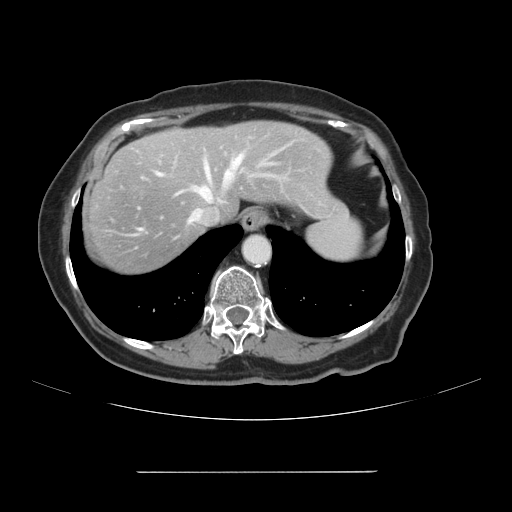
Contrast-enhanced abdominal CT, one axial slice. Position 89 of 111 along the scan axis. 120 kVp. Intravenous contrast given. Soft-tissue window (W 400 / L 40 HU). 2.5 mm slice thickness. 512 × 512 image matrix, field of view 400 × 400 mm. Female patient, age 74 years. Case-level facts recorded for this patient, not image findings: diagnosis: colorectal cancer liver metastases, imaged before liver resection; multiple liver metastases: yes; largest metastasis: 1.1 cm; chemotherapy before resection: yes.
Structures marked on this image (manually delineated by an expert):
- hepatic veins: bounding box [x1, y1, x2, y2] px = [158, 139, 304, 222]
- liver: [83, 121, 342, 276]
- planned liver remnant (the part of the liver to remain after resection): [170, 121, 343, 218]
- portal vein (with intrahepatic branches): [206, 161, 266, 188]